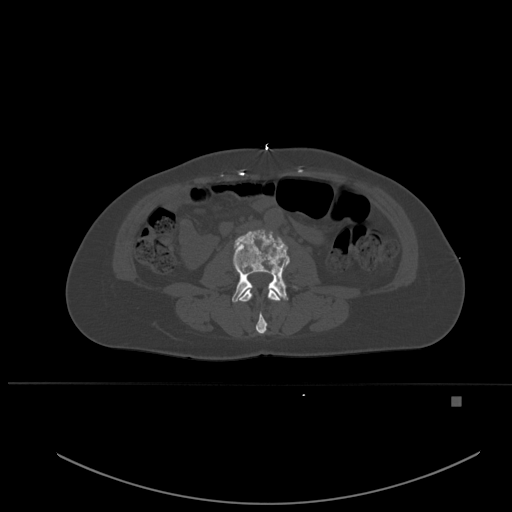
CT including the spine, one axial slice. Slice 199 of 651 in the series (ordered by position). Bone window (W 1800 / L 400 HU). 1.5 mm slice thickness. 512 × 512 image matrix. Patient: female, 49 years. From the clinical record (not read from this slice): primary cancer: breast; vertebrae with lytic lesions (as recorded): L3, T12, L4.
Annotated regions visible in this slice (semi-automatically segmented with operator editing):
- L2 vertebra: bounding box [x1, y1, x2, y2] px = [239, 289, 281, 334]
- L3 vertebra: [232, 231, 290, 303]